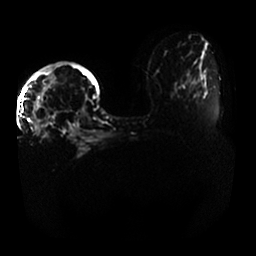
Breast MRI, one axial slice; diffusion-weighted series; image 2 of 4 stored at this slice position (different b-values; order by instance number); 1.5 T; 4 mm slice thickness; 256 × 256 image matrix, field of view 400 × 400 mm. Female patient.
Outlined on this slice (manually delineated by an expert):
- tumour on diffusion-weighted imaging: bounding box [x1, y1, x2, y2] px = [30, 94, 50, 133]